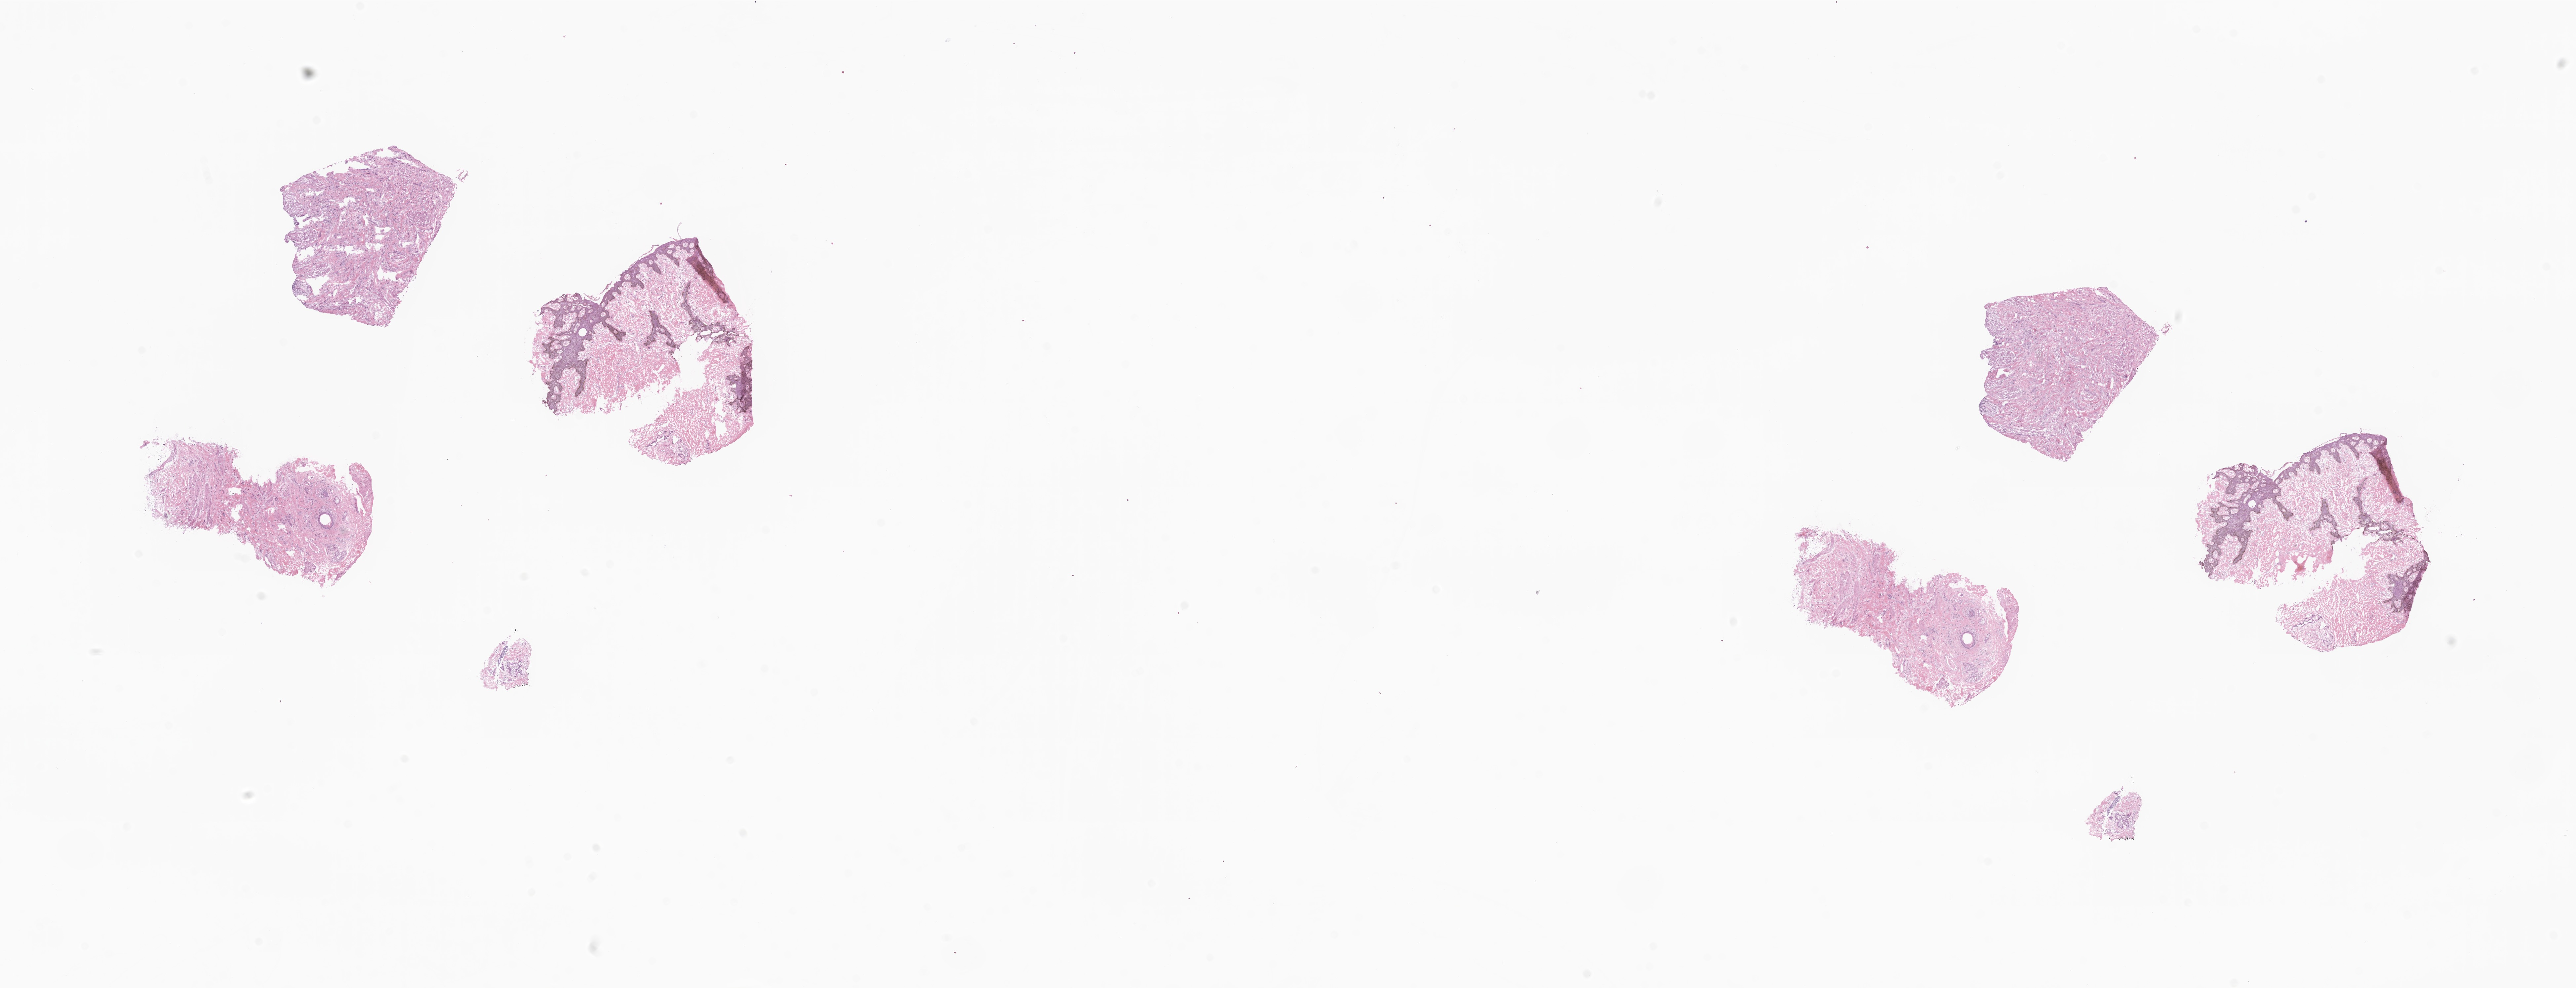
Whole-slide image, hematoxylin and eosin (H&E) stain — low-resolution overview of the scanned area, about 32.9 x 12.6 mm, cryosection, primary tumor, anatomic site: breast (right). Female patient; age at initial diagnosis 64 years.
Histologic diagnosis: Metaplastic carcinoma, NOS.